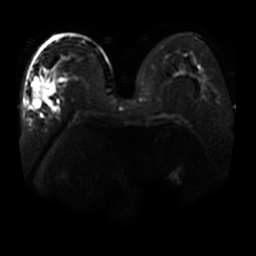
Breast MRI, one axial slice; position 23 of 44 along the scan axis; diffusion-weighted series; image 2 of 4 stored at this slice position (different b-values; order by instance number); 3 T; 5 mm slice thickness; 256 × 256 image matrix. Female patient.
Structures marked on this image (manually delineated by an expert):
- tumour on diffusion-weighted imaging: bounding box <33,78,55,107> (left, top, right, bottom; pixels)